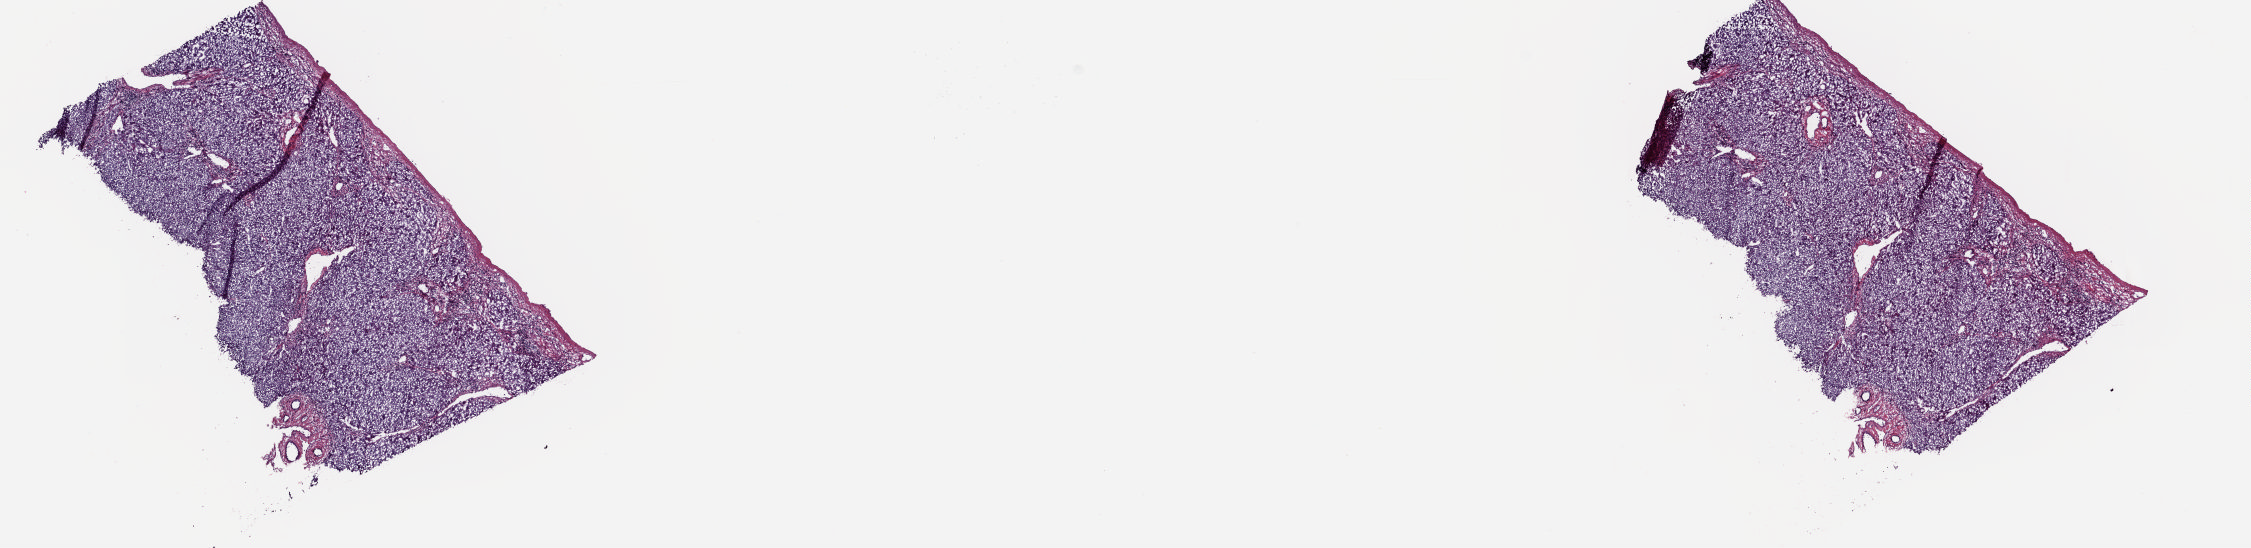
Whole-slide histology image, H&E — a low-resolution overview of the entire scanned area, about 17.9 x 4.3 mm. Frozen section from the top of the tissue portion. Sample: solid tissue normal (non-tumour tissue), liver. Male, age 54 years at initial diagnosis. Pathologist review of this section (percent, as recorded): tumour cells 0%, tumour nuclei 0%, normal cells 85%, stromal cells 15%, necrosis 0%. Inflammatory infiltration, as recorded: lymphocyte infiltration 3%, monocyte infiltration 0%, neutrophil infiltration 0%.
This section: solid tissue normal (non-tumour) sample from the same patient. Patient diagnosis: Hepatocellular carcinoma, NOS.